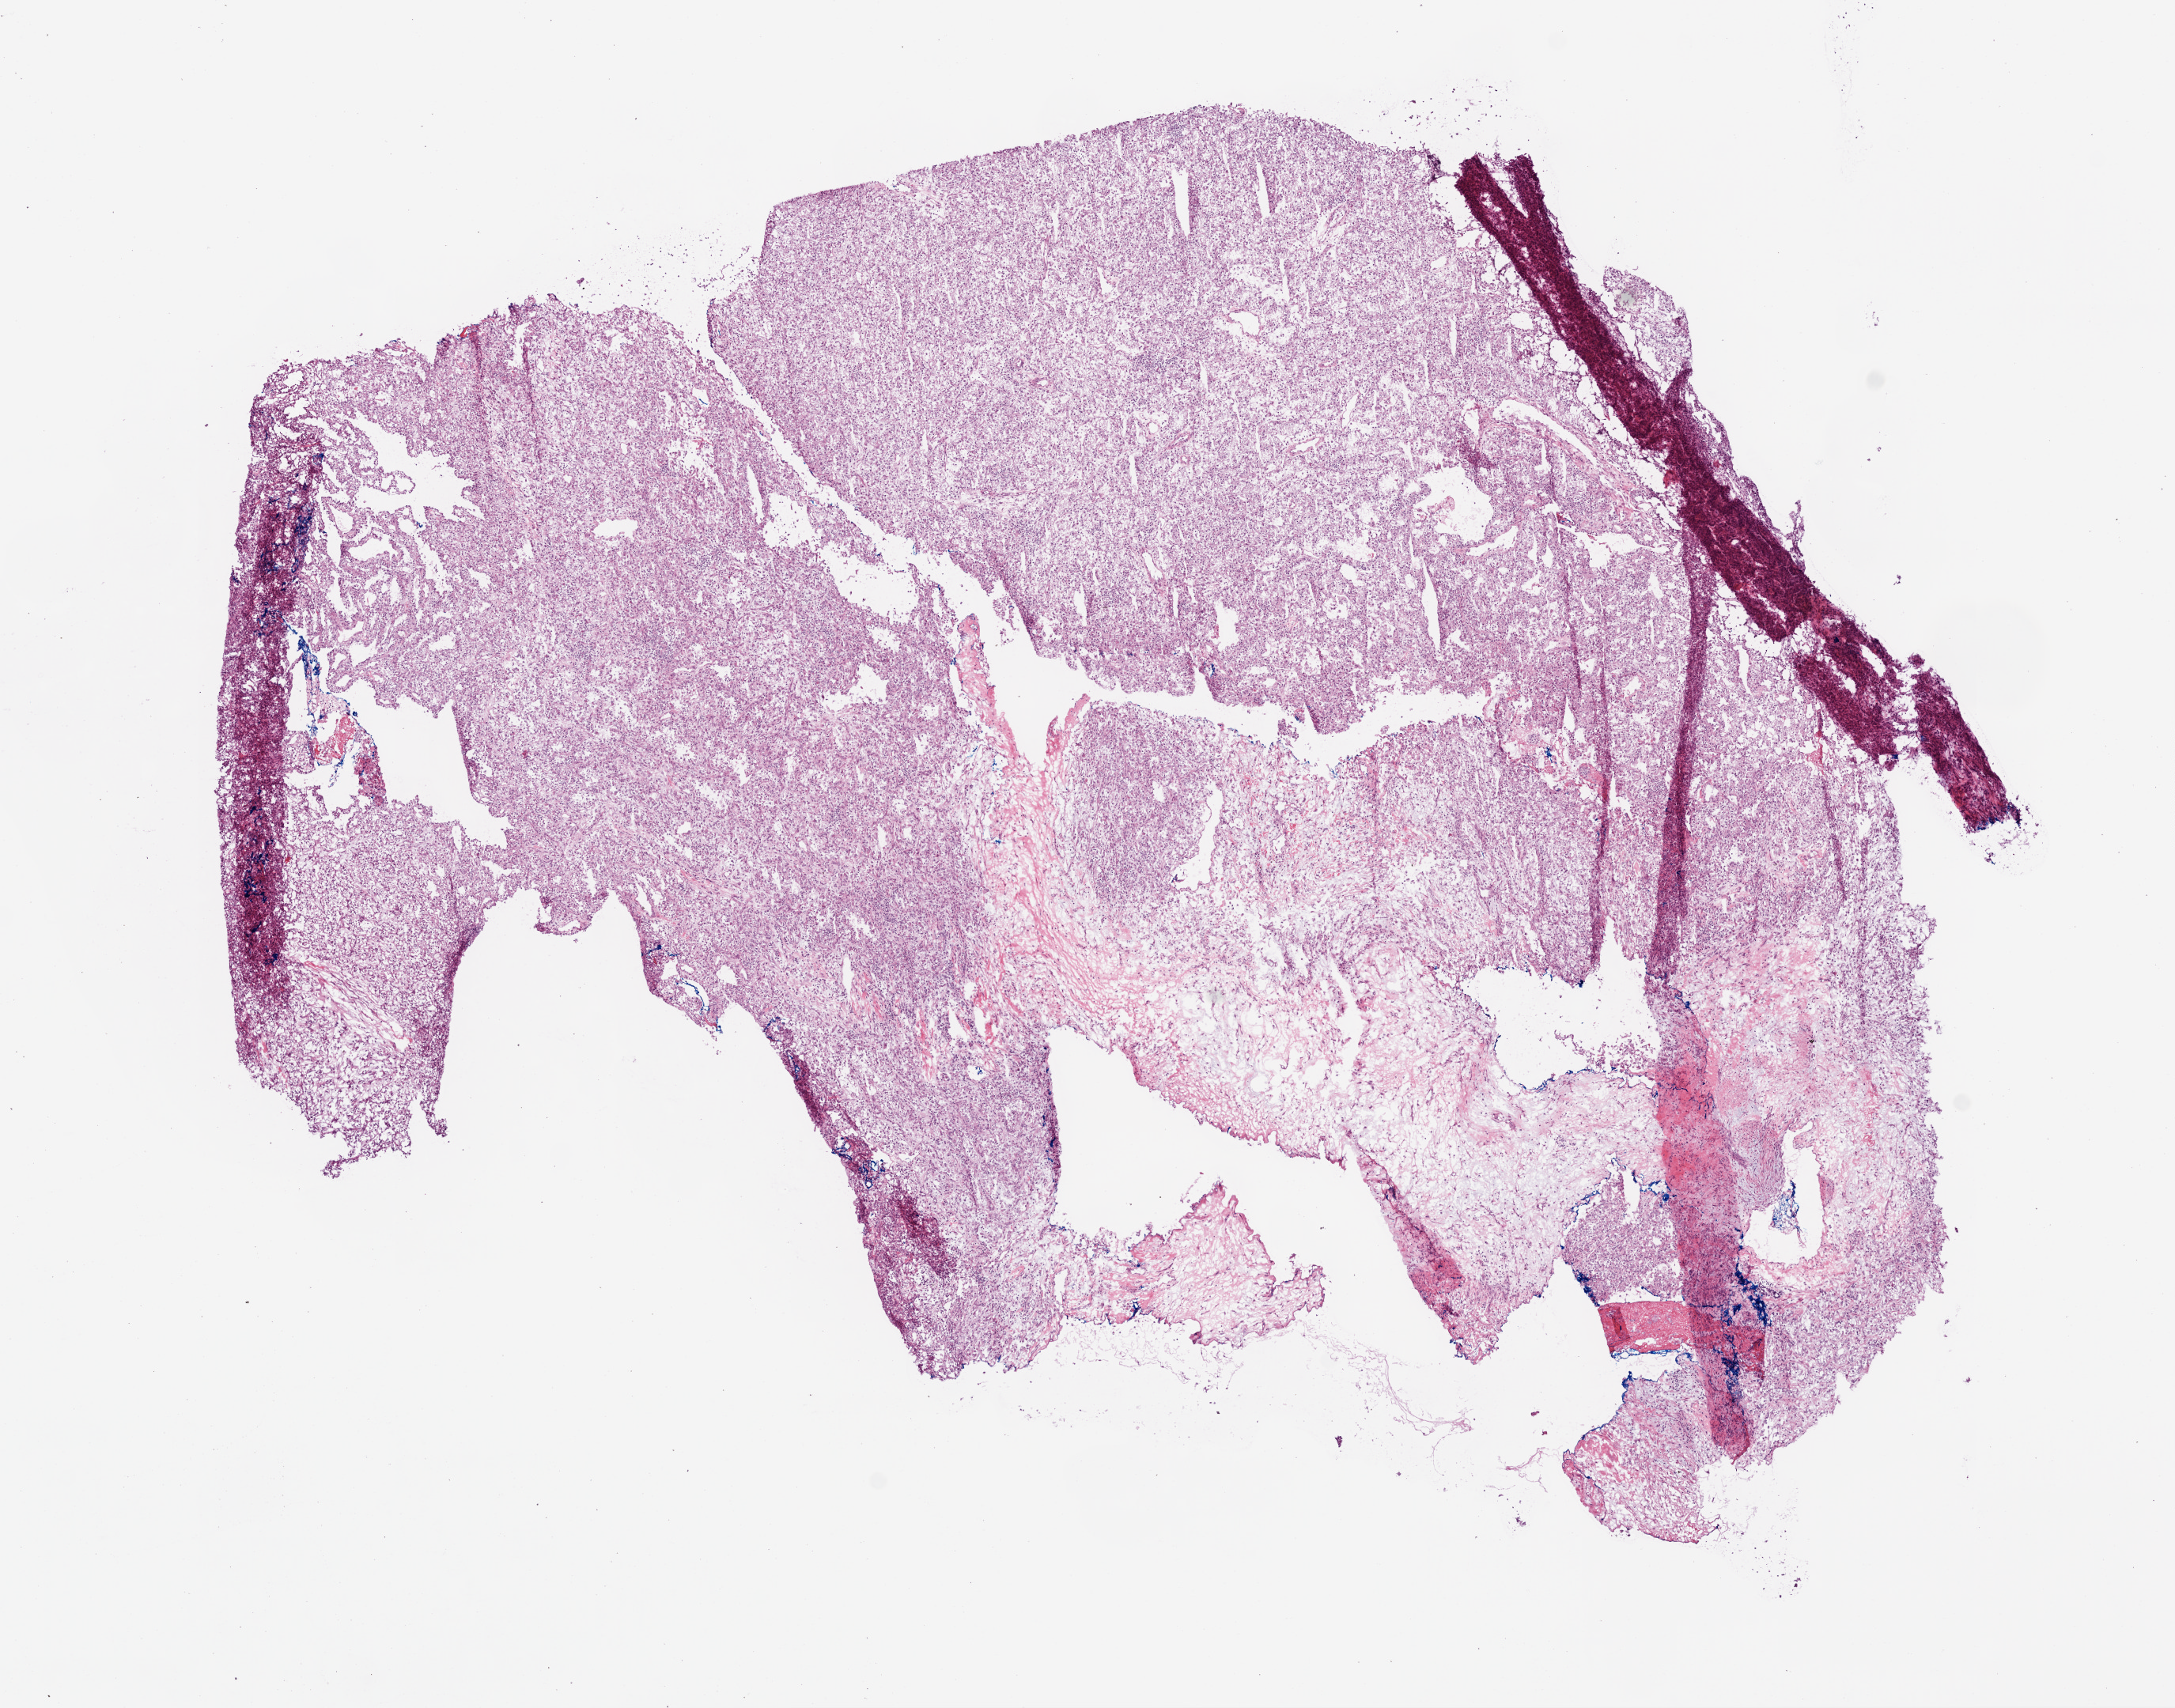
Whole-slide histology image, H&E-stained — low-resolution overview of the scanned area, about 11.0 x 8.7 mm (acquisition: 20x scan), frozen section from the top of the tissue portion, sample: primary tumour, kidney. Female, age 63 years at initial diagnosis. Histologic grade: G3 (poorly differentiated). Pathologist review of this section (percent, as recorded): tumour cells 85%, tumour nuclei 80%, normal cells 0%, stromal cells 15%, necrosis 0%.
AJCC pathologic stage: III (7th edition). Laterality: right. Histologic diagnosis: Clear cell adenocarcinoma, NOS.